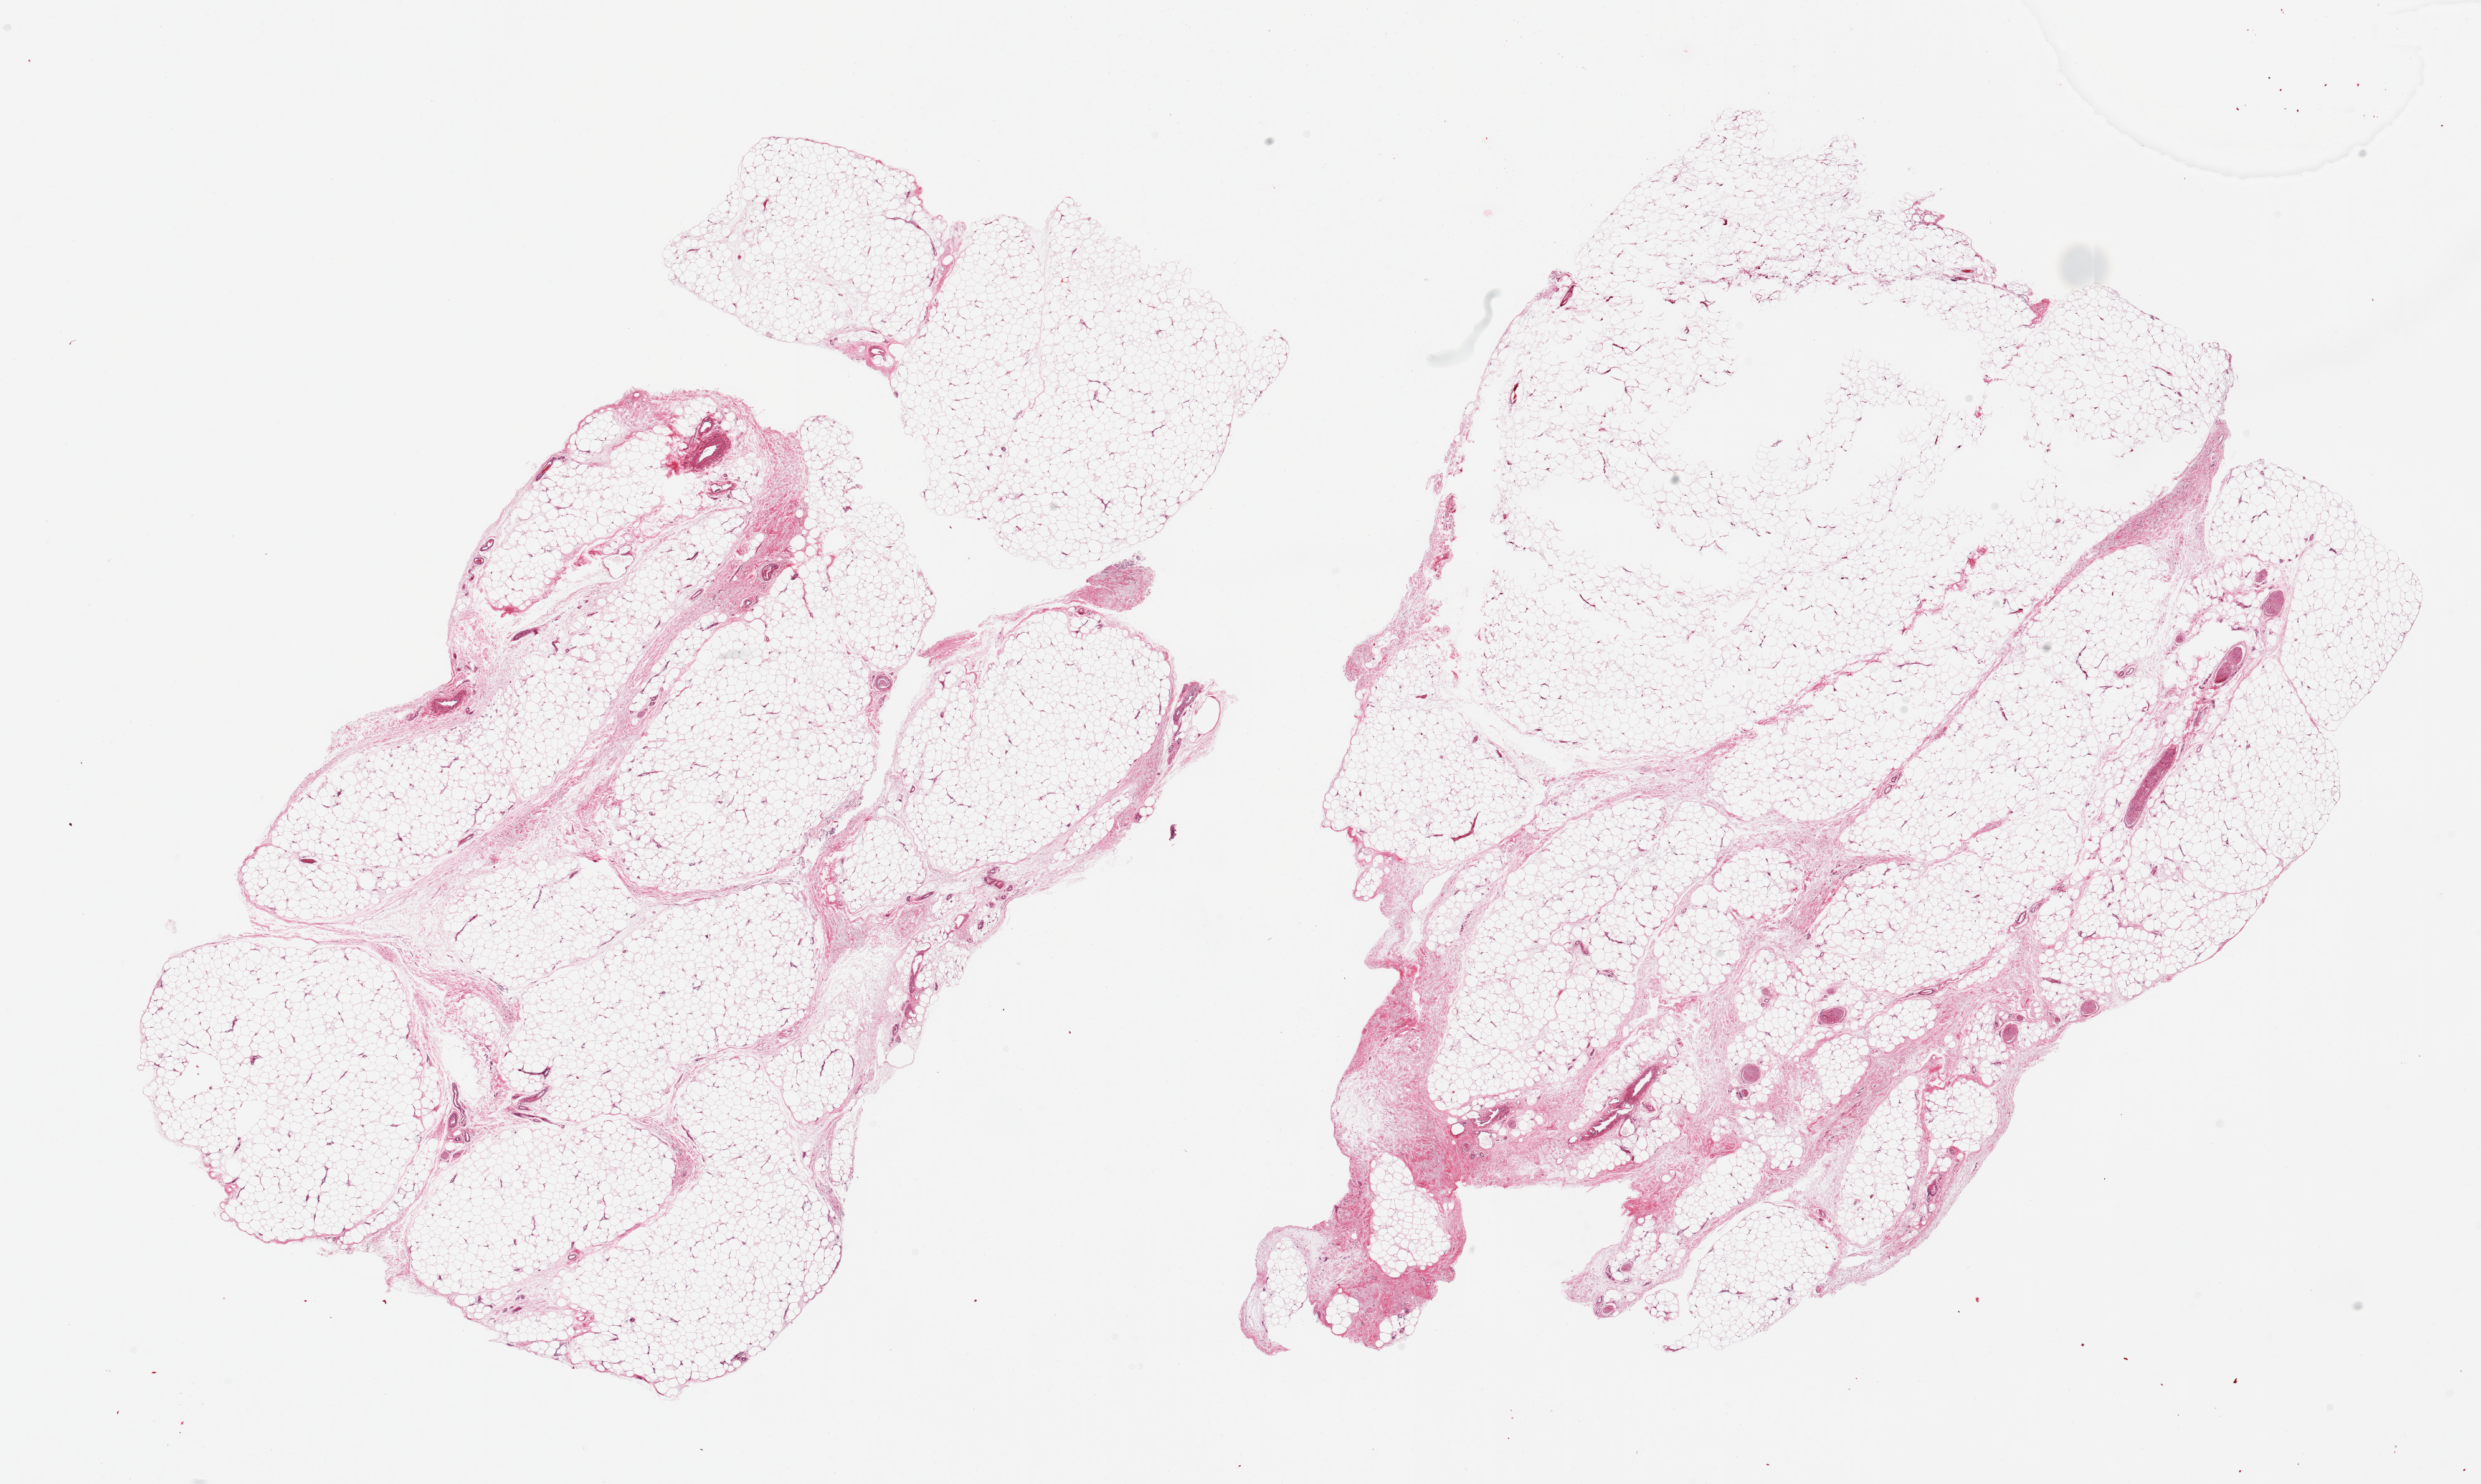
Haematoxylin and eosin whole-slide image, a low-resolution overview of the entire scanned area, about 31.5 x 18.8 mm. PAXgene-fixed paraffin-embedded (PFPE) section. Sampled site (target tissue): adipose tissue. Tissue donor sample.
• reviewer comment on this tissue sample: 2 pieces, ~10-15% fascia/vascular elements